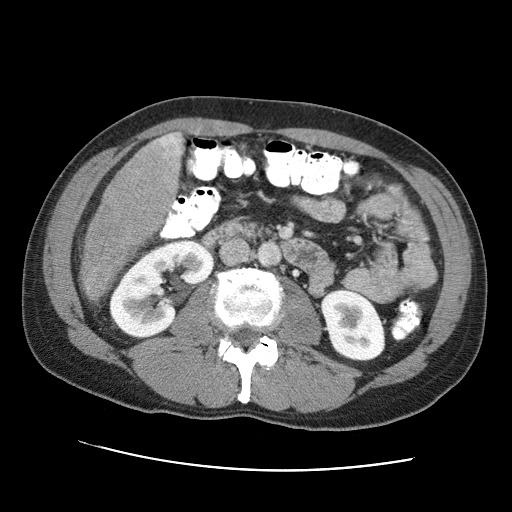
Contrast-enhanced abdominal CT (liver protocol), one axial slice. Position 17 of 95 along the scan axis. Reconstruction kernel STANDARD. 120 kVp. One of 2 acquisitions stored at this slice position. Soft-tissue window (W 400 / L 40 HU). 2.5 mm slice thickness. 512 × 512 image matrix, field of view 360 × 360 mm. Case-level facts recorded for this patient, not image findings: diagnosis: hepatocellular carcinoma (patient treated with transarterial chemoembolisation; whether this scan precedes or follows treatment is not stated here); TNM stage (as recorded): Stage-IVA; Child-Pugh class: A; tumour differentiation: moderately differentiated.
Structures marked on this image (semi-automatic segmentation, software-assisted and operator-edited):
- liver parenchyma outside the tumour (the mass and vessels are separate outlines, so this box may not span the whole liver): bounding box (x1, y1, x2, y2) in pixels: (157, 132, 182, 193)
- mass: (78, 133, 180, 302)
- liver vessels: (178, 151, 181, 155)